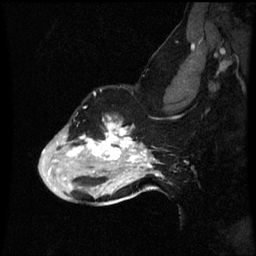
Breast MRI (dynamic contrast-enhanced), one sagittal slice. Slice 43 of 60 in the series (ordered by position). Dynamic contrast-enhanced series, image 2 of 3 at this slice position (ordered by acquisition). 1.5 T. TE 4.2 ms, TR 8.9 ms. 2 mm slice thickness. 256 × 256 image matrix, field of view 200 × 200 mm. Patient: female, 49 years. From the clinical record (not read from this slice): setting: breast cancer imaged before/during neoadjuvant chemotherapy; receptor status: HR-positive, HER2-negative.
Outlined on this slice (semi-automatic segmentation, software-assisted and operator-edited):
- analysis volume of interest (the breast-tissue region the enhancement analysis was run in; not a lesion): box from (x=40, y=116) to (x=159, y=199) px
- tumour enhancement mask (voxels above the 70 % enhancement threshold inside the analysis volume of interest): (x=68, y=122)–(x=159, y=177)